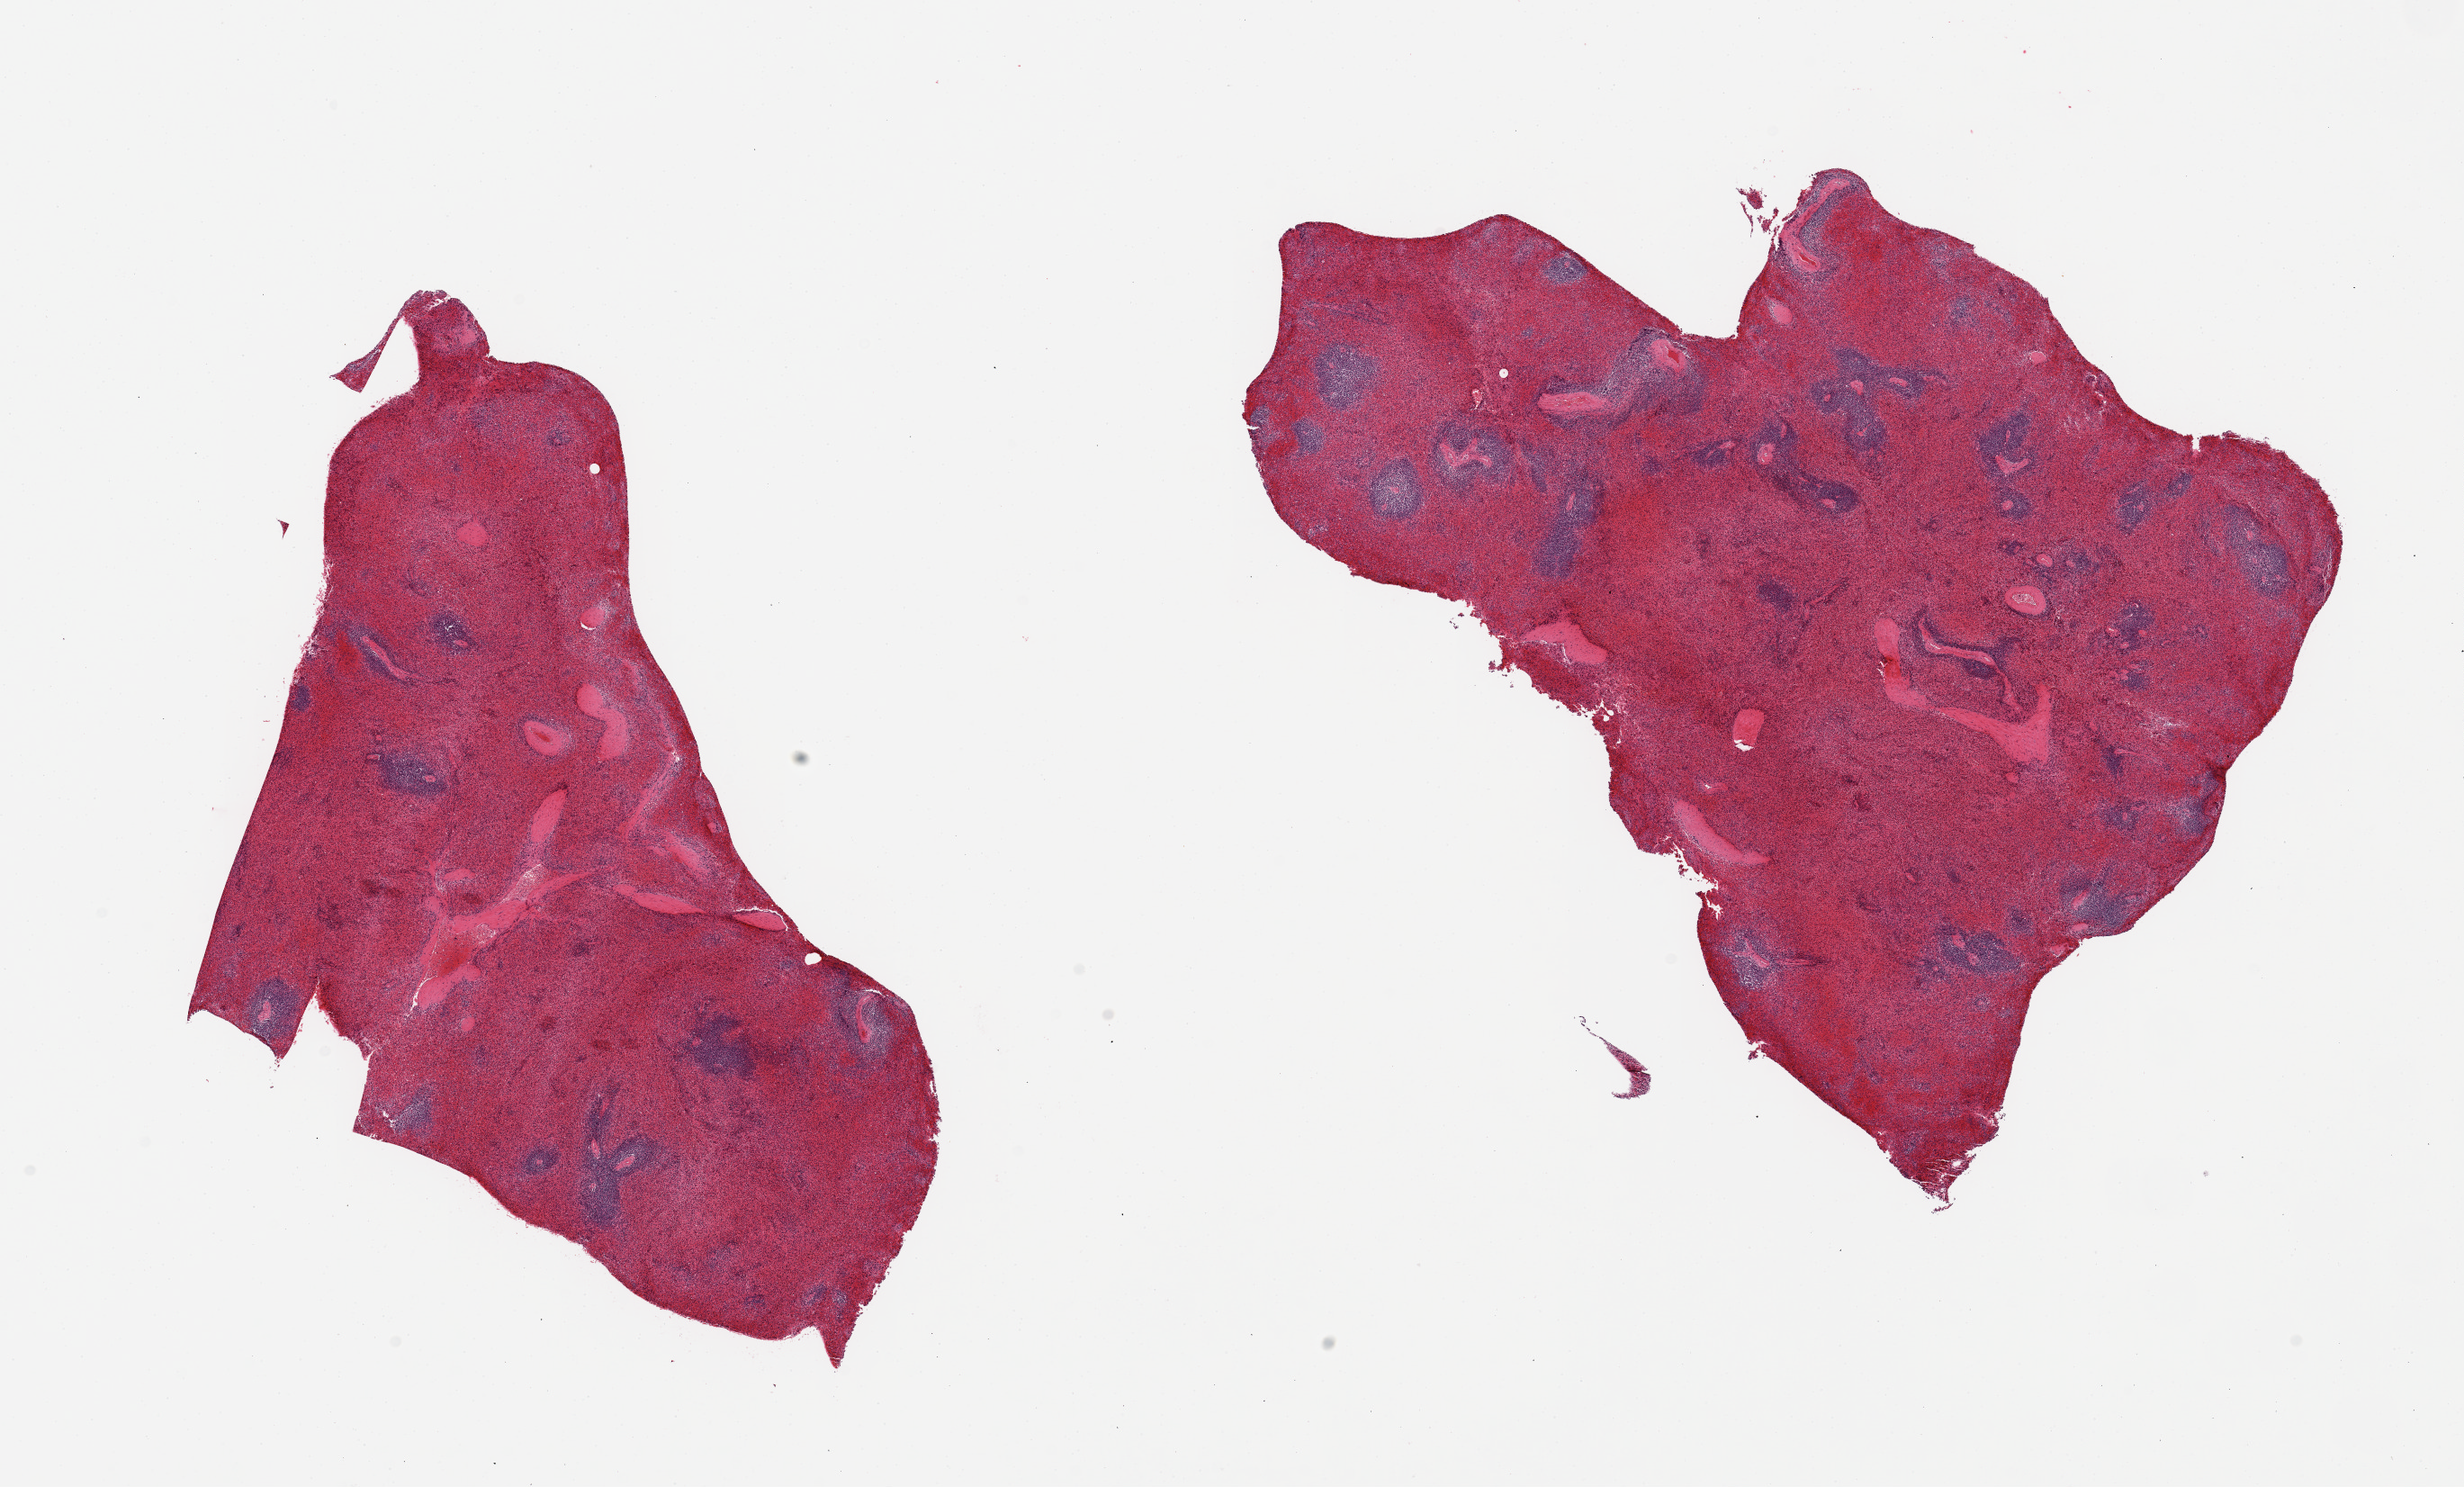
Whole-slide image, haematoxylin and eosin stain, brightfield, whole scanned area (about 21.7 x 13.1 mm) shown as a low-resolution overview. PAXgene-fixed, paraffin-embedded tissue. Sampled site (target tissue): spleen. Tissue donor sample. Donor: male.
Reviewer comment on this tissue sample: 2 pieces; congested.